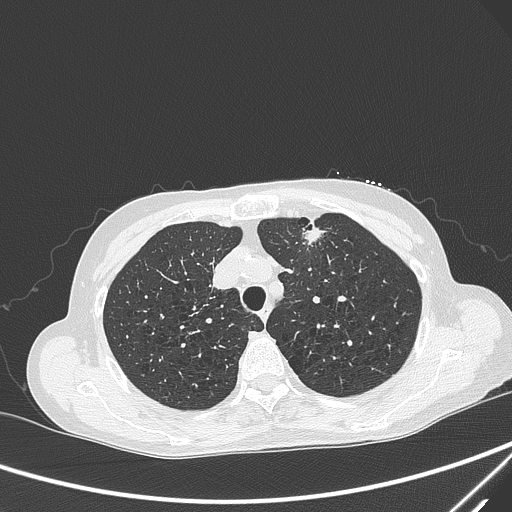
Chest CT, one axial slice; slice 234 of 299 in the series (ordered by position); lung window (W 1500 / L -600 HU); 512 × 512 image matrix. Female patient, age 71 years. From the clinical record (not read from this slice): clinical TNM (as recorded): T1c N0 M0; histopathological grade: G2-3.
Annotated regions visible in this slice (bounding box drawn by a radiologist):
- lung tumour (recorded histology: adenocarcinoma): bounding box [x1, y1, x2, y2] px = [298, 219, 332, 254]